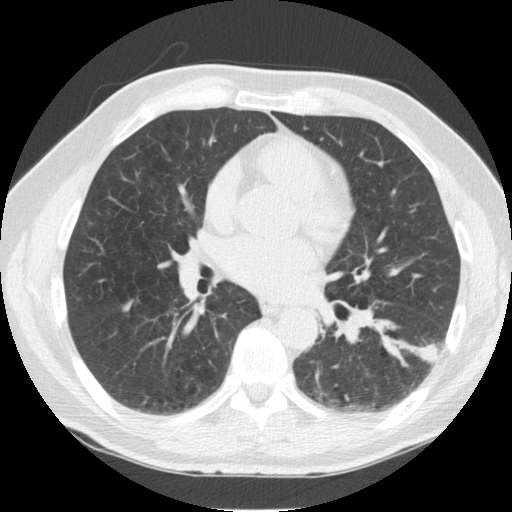
Low-dose screening chest CT, one axial slice. Reconstruction kernel STANDARD. Lung window (W 1500 / L -600 HU). 2.5 mm slice thickness. 512 × 512 image matrix, field of view 344 × 344 mm.
Outlined on this slice (manually delineated by an expert):
- lesion 1 (tumor, lower lobe of left lung): box from (x=415, y=343) to (x=438, y=363) px